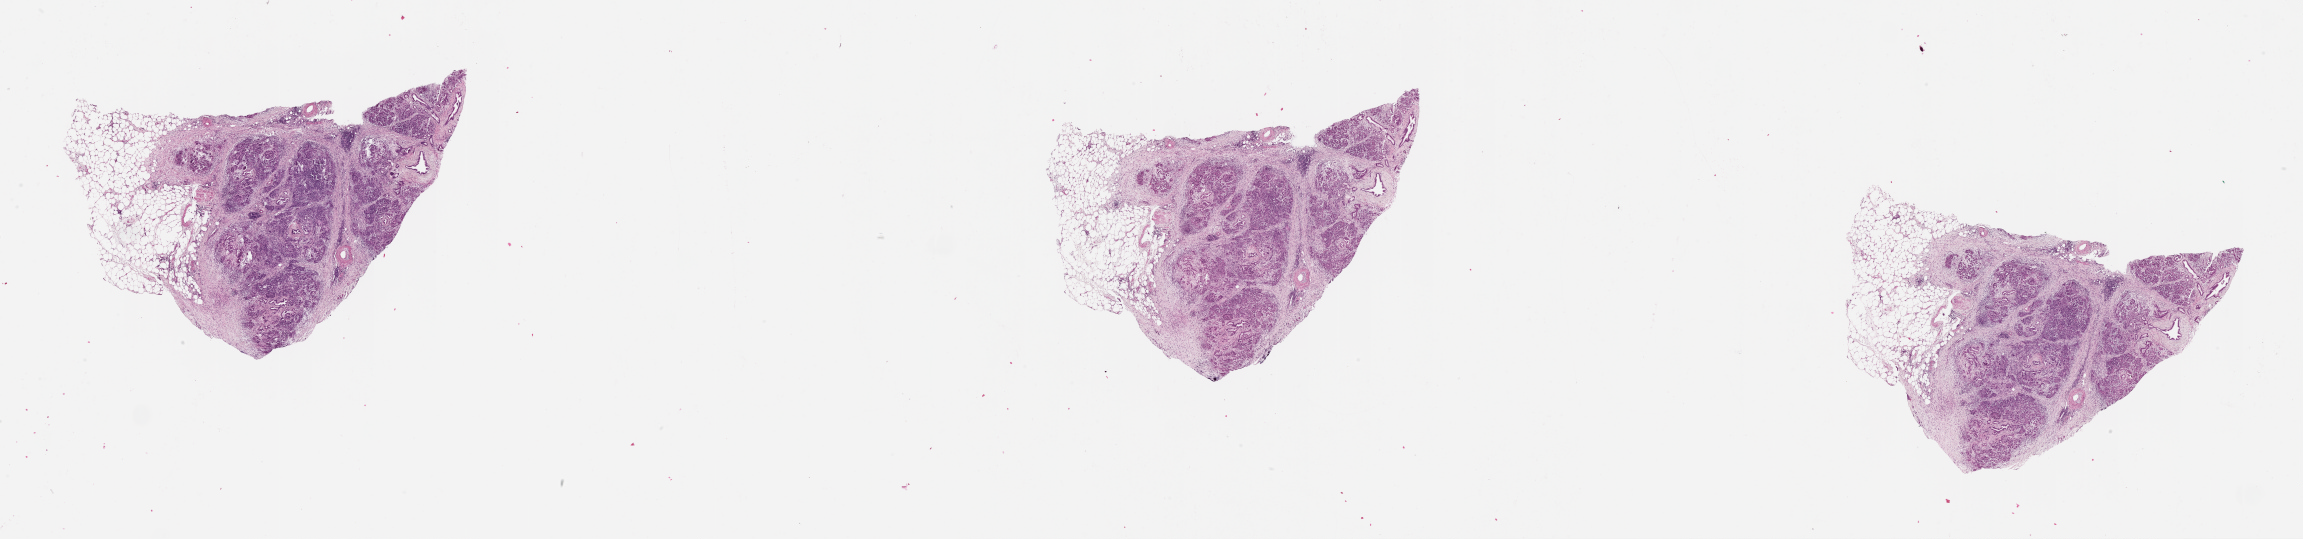
Whole-slide histology image, H&E-stained — whole scanned area (about 37.1 x 8.7 mm, slide scanned at 20x) shown as a low-resolution overview, pancreas, tumour tissue. Male, 77 y/o.
Patient diagnosis (cohort enrolment): ductal adenocarcinoma (pancreas).